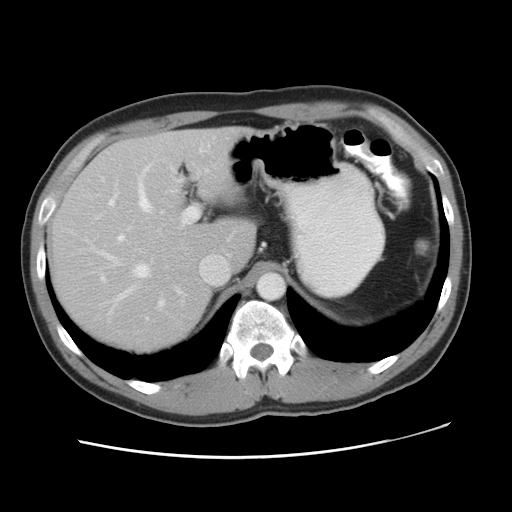
Contrast-enhanced abdominal CT, one axial slice; slice 34 of 49 in the series (ordered by position); intravenous contrast given; soft-tissue window (W 400 / L 40 HU); 5 mm slice thickness; 512 × 512 image matrix, field of view 363 × 363 mm. Male patient, age 41 years. Case-level facts recorded for this patient, not image findings: diagnosis: colorectal cancer liver metastases, imaged before liver resection; multiple liver metastases: yes; largest metastasis: 0.7 cm; disease in both lobes: yes.
Annotated regions visible in this slice (outlined manually by an expert reader):
- hepatic veins: bounding box [x1, y1, x2, y2] px = [97, 164, 228, 307]
- liver: [50, 128, 256, 354]
- planned liver remnant (the part of the liver to remain after resection): [100, 128, 255, 269]
- portal vein (with intrahepatic branches): [100, 180, 199, 292]